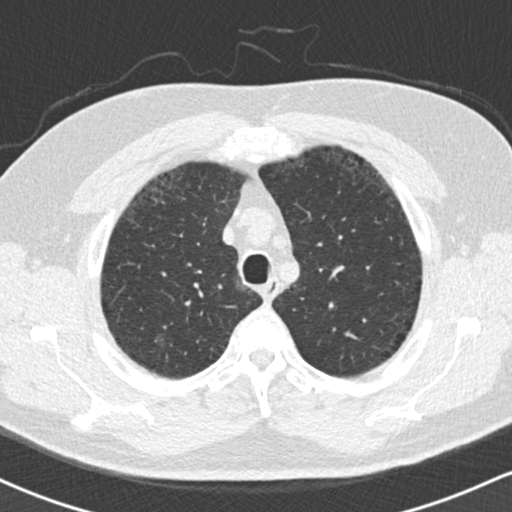
Axial slice from a low-dose chest CT screening exam; second screening round (one year after baseline); lung window (W 1500 / L -600 HU); 512 × 512 image matrix. Male, age 59 years at enrolment. Current smoker at enrolment.
Lesion marked by an expert reader, box from (x=151, y=316) to (x=201, y=366) px. Reader record for this screening exam (exam-level; its link to the box is not recorded): non-calcified nodule or mass ≥4 mm, right upper lobe, 18 × 16 mm, ground glass attenuation, pre-existing on the prior screen: yes. Participant outcome: lung cancer diagnosed 60 days after this screen — bronchiolo-alveolar adenocarcinoma, NOS, right lower lobe, stage IA (AJCC 6th edition), 15 mm at pathology.